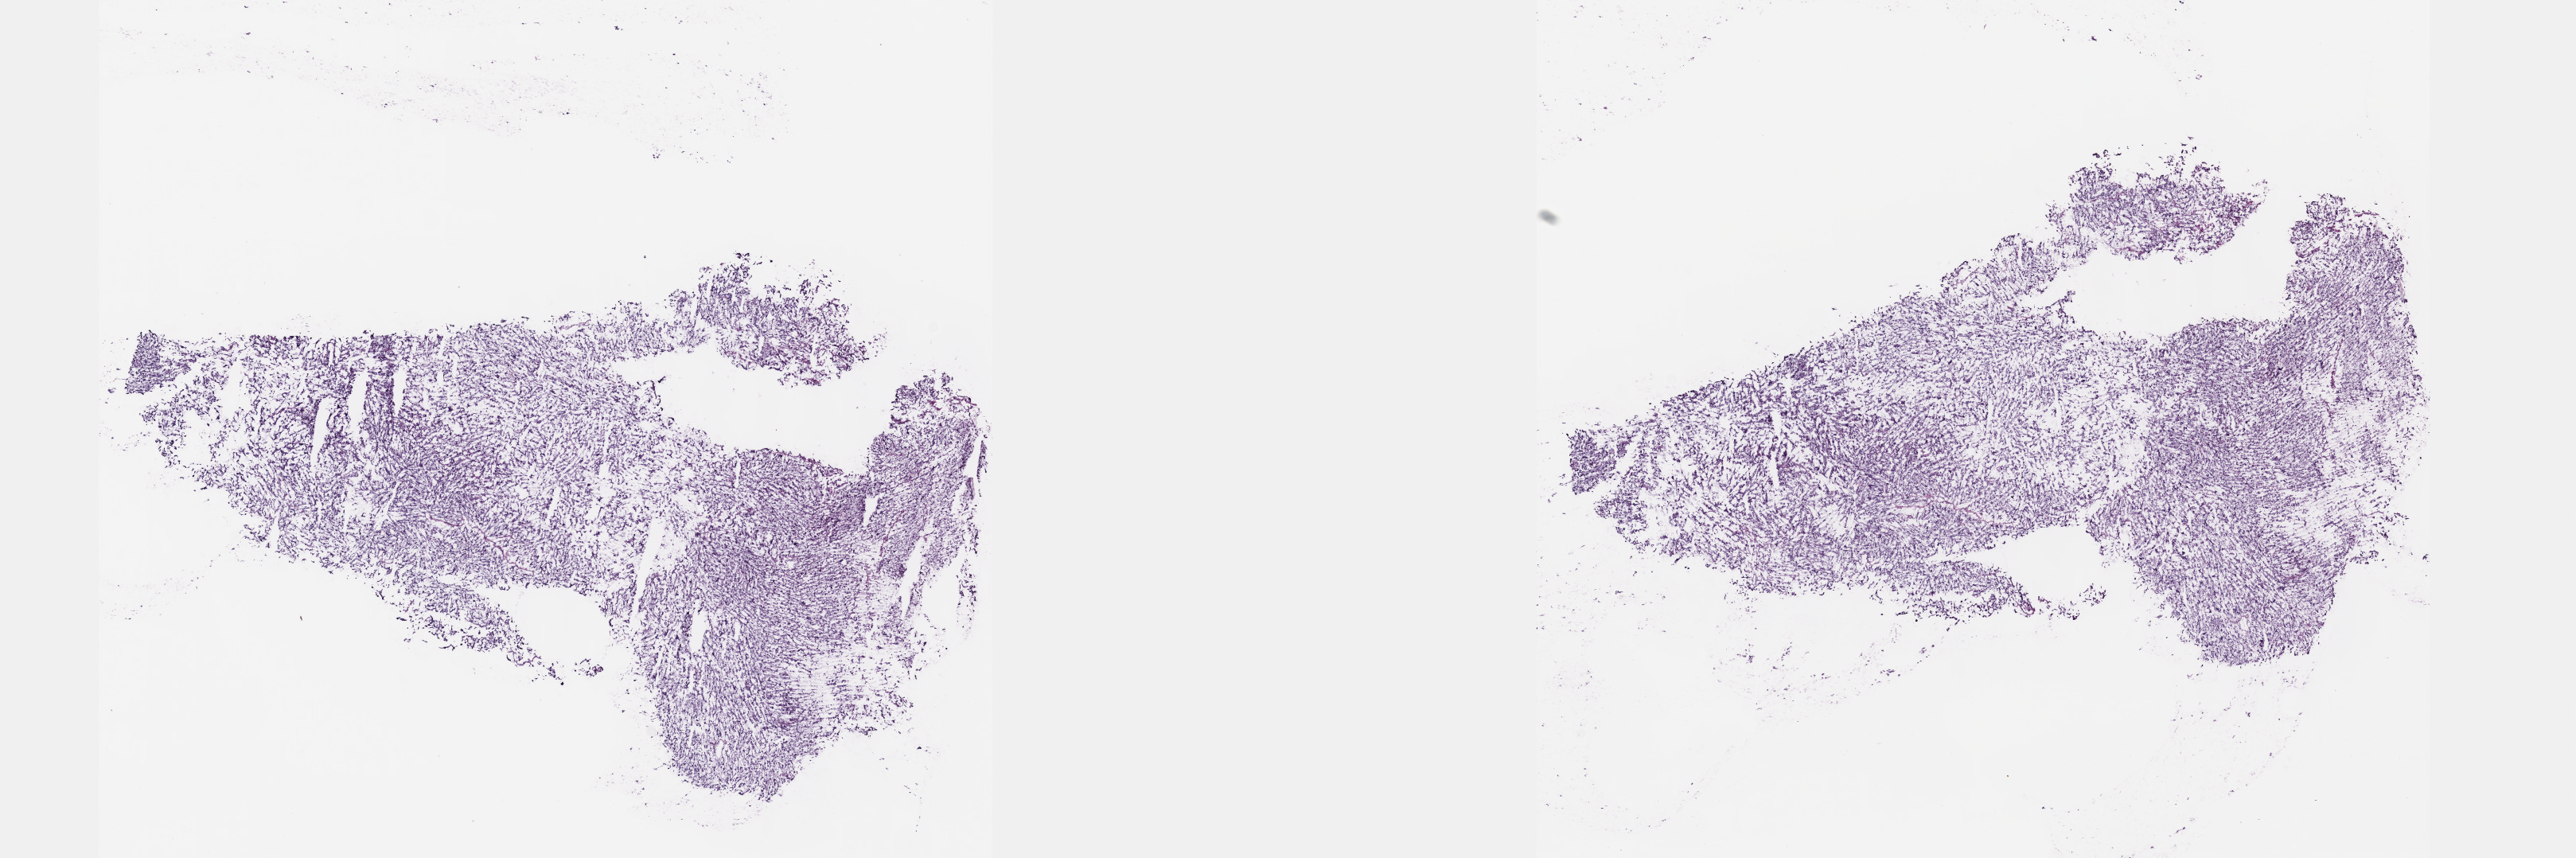
Whole-slide histology image, H&E, low-resolution overview of the scanned area, about 26.2 x 8.7 mm; frozen section from the top of the tissue portion; adrenal gland, primary tumour sample. Male patient; age at initial diagnosis 40 years. Composition of this section per pathologist review: tumour cells 99%, tumour nuclei 99%, normal cells 0%, stromal cells 1%, necrosis 0%. Infiltration values recorded for this section: lymphocyte infiltration 0%, monocyte infiltration 0%, neutrophil infiltration 0%.
Histologic diagnosis: Pheochromocytoma, malignant.